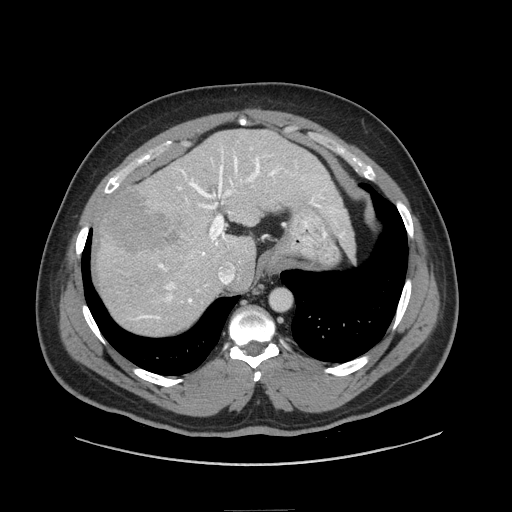
Contrast-enhanced abdominal CT (liver protocol), one axial slice. Slice 59 of 87 in the series (ordered by position). Reconstruction kernel STANDARD. 140 kVp. Soft-tissue window (W 400 / L 40 HU). 2.5 mm slice thickness. 512 × 512 image matrix, field of view 440 × 440 mm. Case-level facts recorded for this patient, not image findings: diagnosis: hepatocellular carcinoma (patient treated with transarterial chemoembolisation; whether this scan precedes or follows treatment is not stated here); TNM stage (as recorded): Stage-II; Child-Pugh class: A; tumour differentiation: moderately differentiated; tumour nodularity: uninodular.
Annotated regions visible in this slice (semi-automatic segmentation, software-assisted and operator-edited):
- liver parenchyma outside the tumour (the mass and vessels are separate outlines, so this box may not span the whole liver): bounding box <96,130,342,334> (left, top, right, bottom; pixels)
- mass: <96,189,179,255>
- liver vessels: <138,148,338,319>